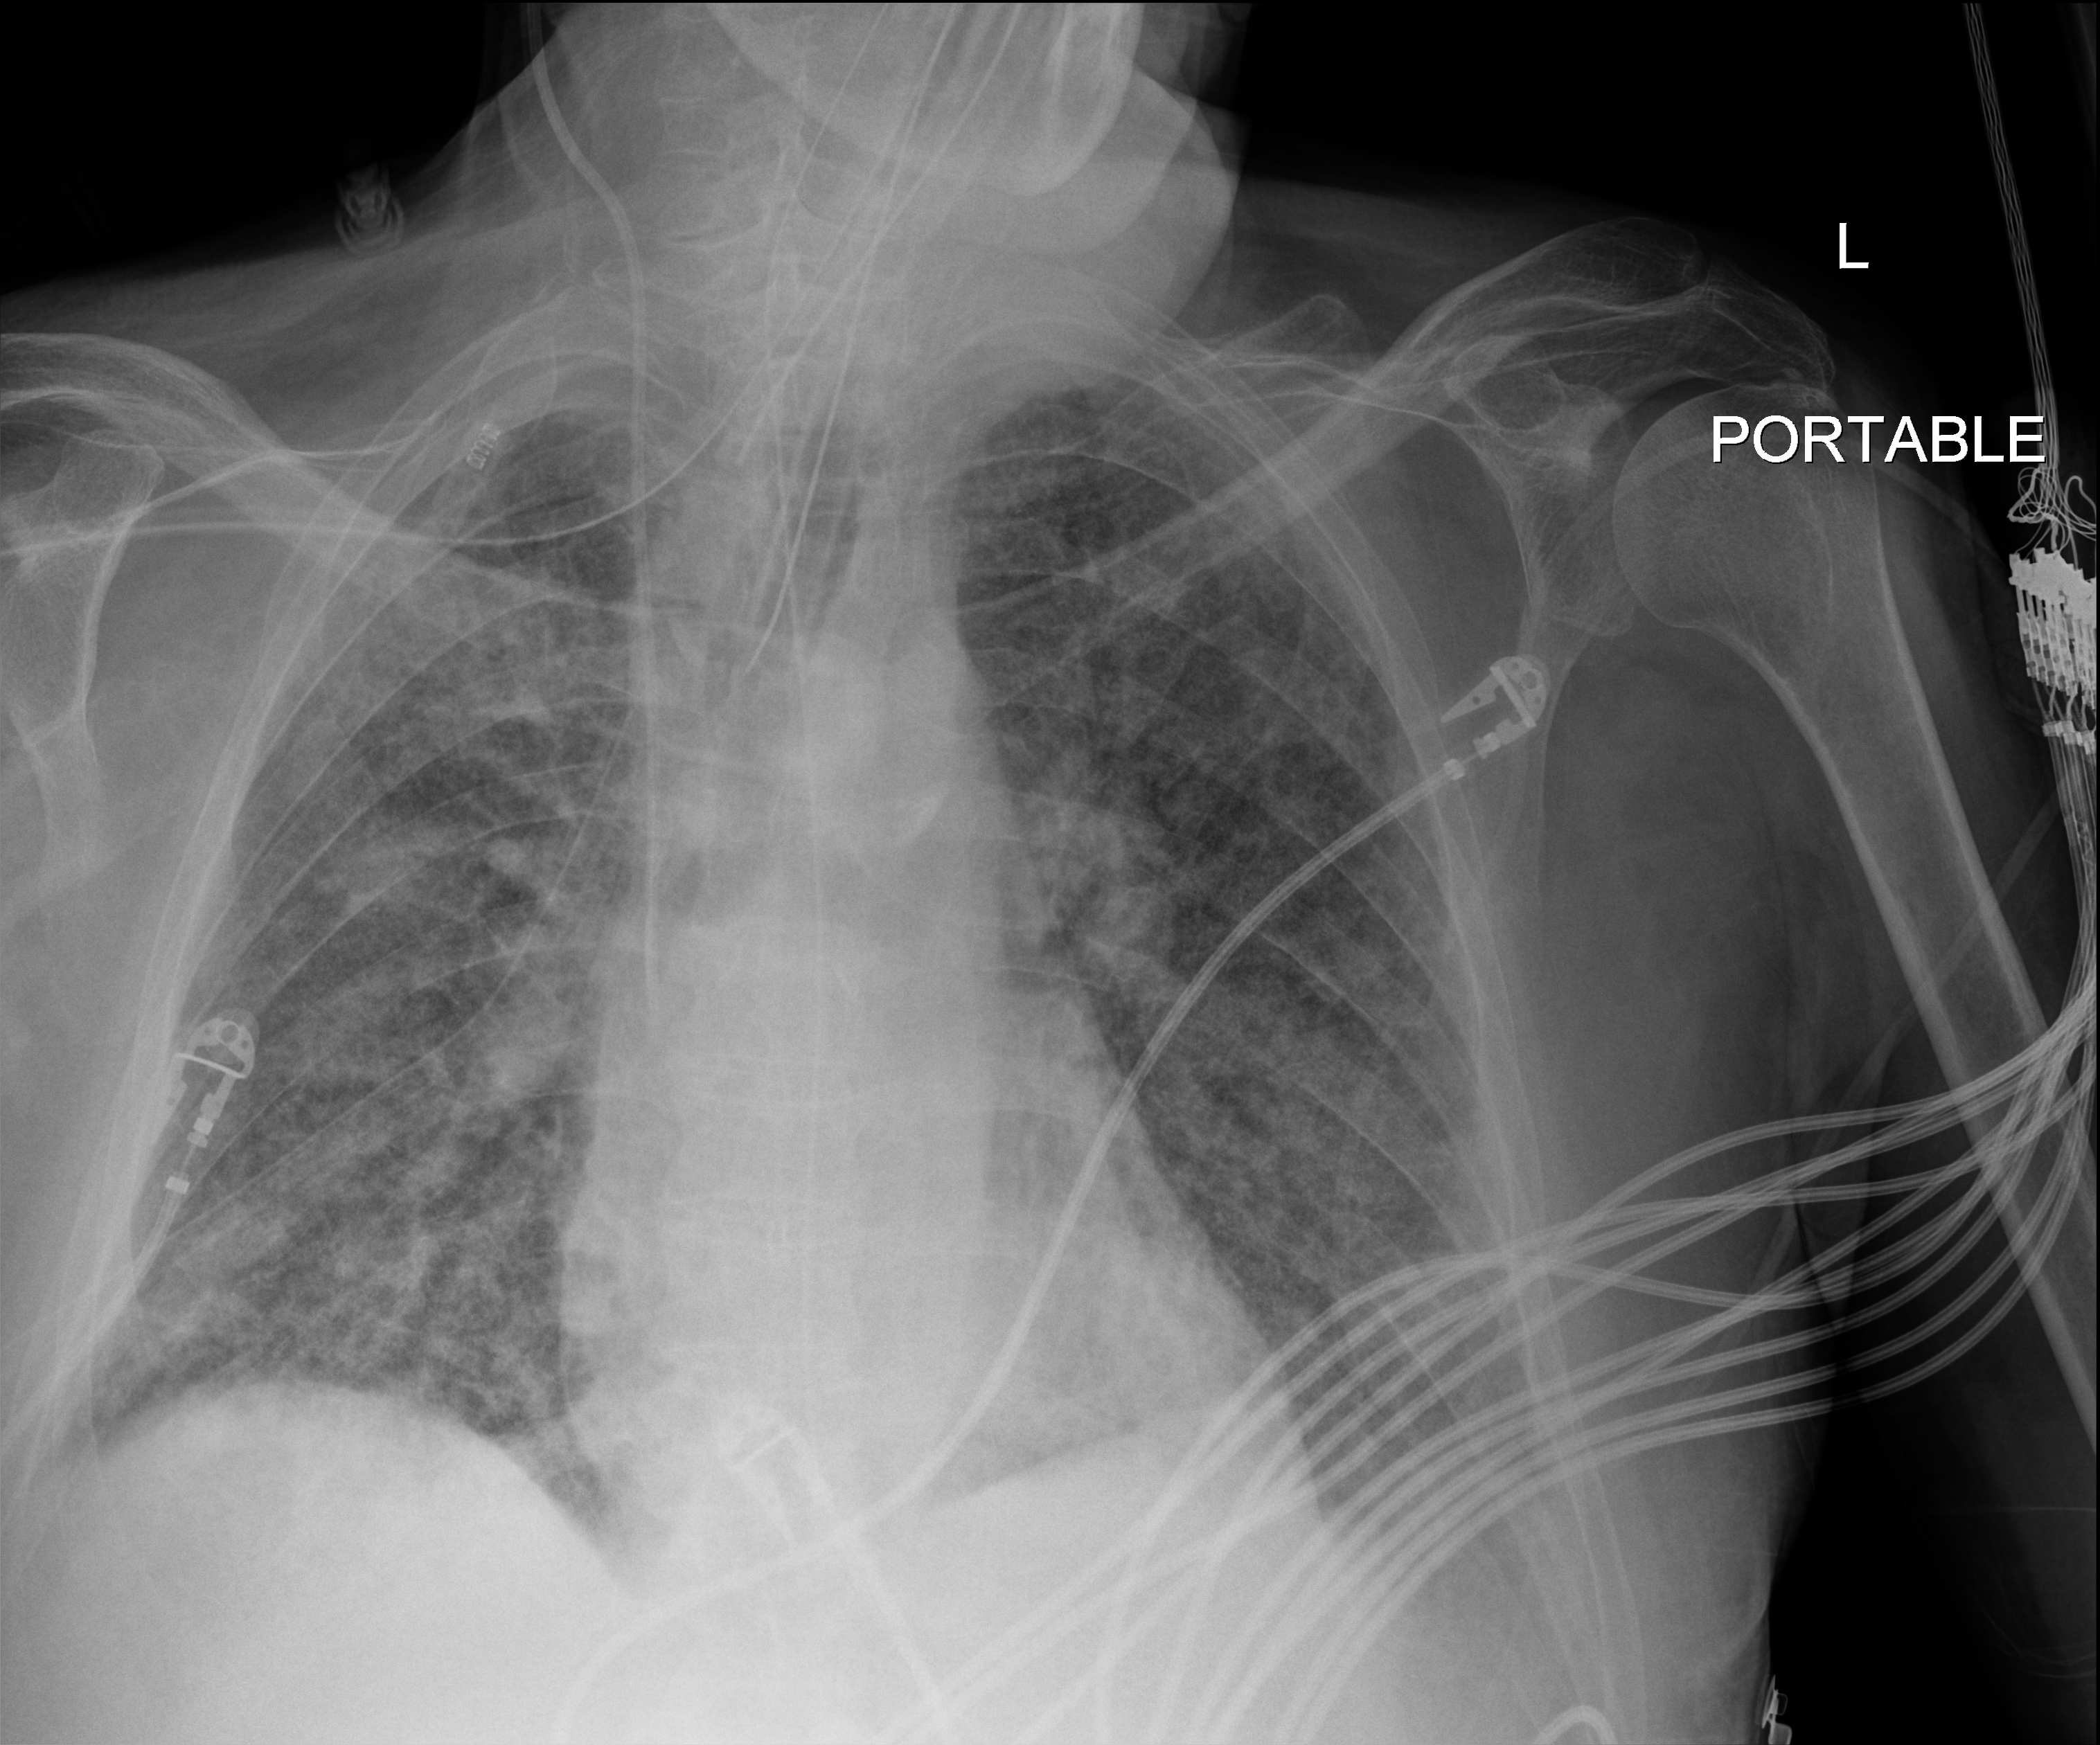
Bedside chest radiograph (digital radiography). Patient hospitalised with COVID-19; male, aged 60–74 years.
Admission-level facts for this patient (not findings on this image; timing relative to this image not recorded): admitted to intensive care during this hospital stay: yes.